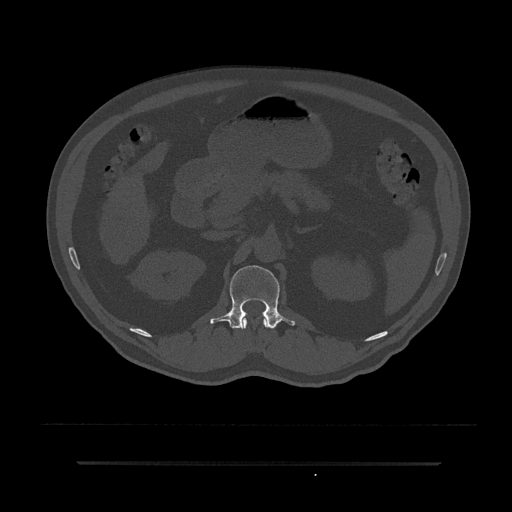
CT including the spine, one axial slice; slice 160 of 797 in the series (ordered by position); reconstruction kernel Br40s/3; 120 kVp; bone window (W 1800 / L 400 HU); 0.5 mm slice thickness; 512 × 512 image matrix, field of view 464 × 464 mm. Male patient, age 59 years. Case-level facts recorded for this patient, not image findings: primary cancer: bile ducts; vertebrae with lytic lesions (as recorded): T10.
Annotated regions visible in this slice (semi-automatic segmentation, software-assisted and operator-edited):
- L1 vertebra: bounding box (x1, y1, x2, y2) in pixels: (210, 265, 295, 329)
- T12 vertebra: (240, 315, 268, 329)